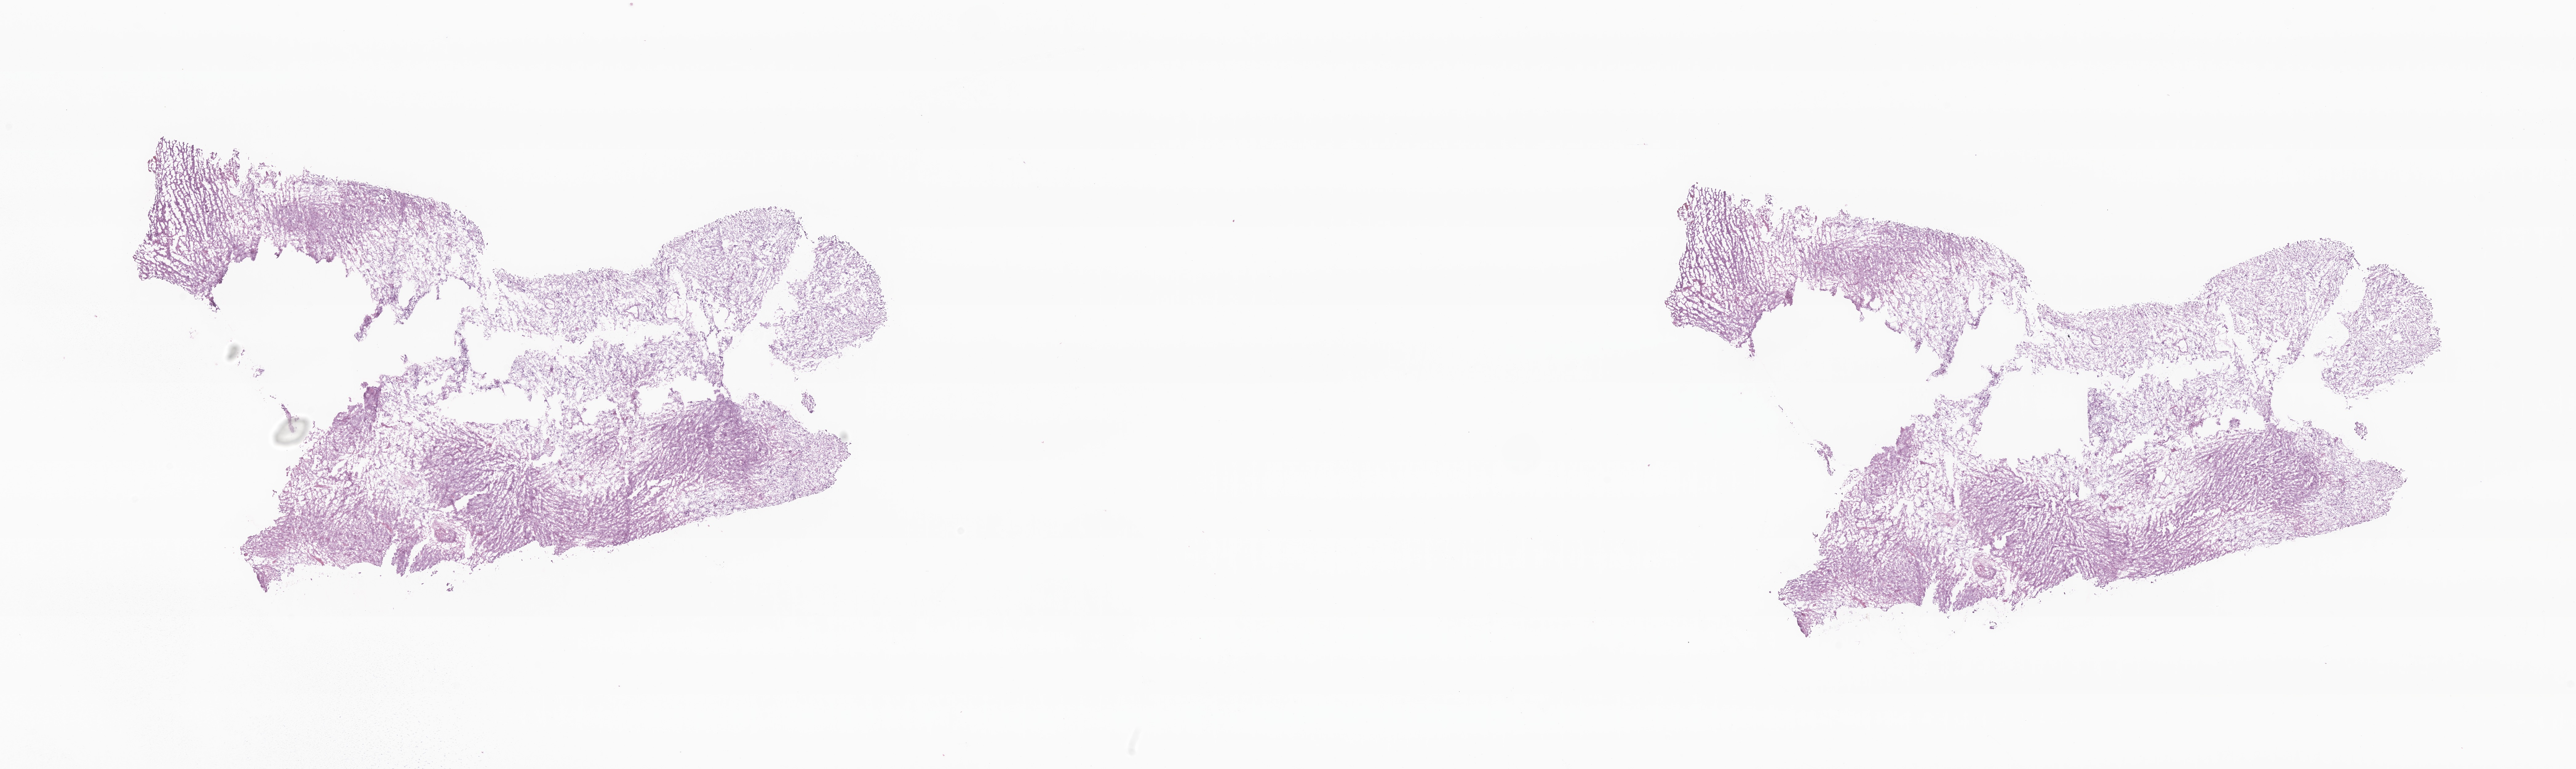
H&E whole-slide image of tumor tissue from the brain, a low-resolution overview of the entire scanned area, about 35.3 x 10.5 mm; frozen section. Male patient, age 103 months (8 years 7 months).
• diagnosis (ICD-O-3 morphology term): Astrocytoma, NOS